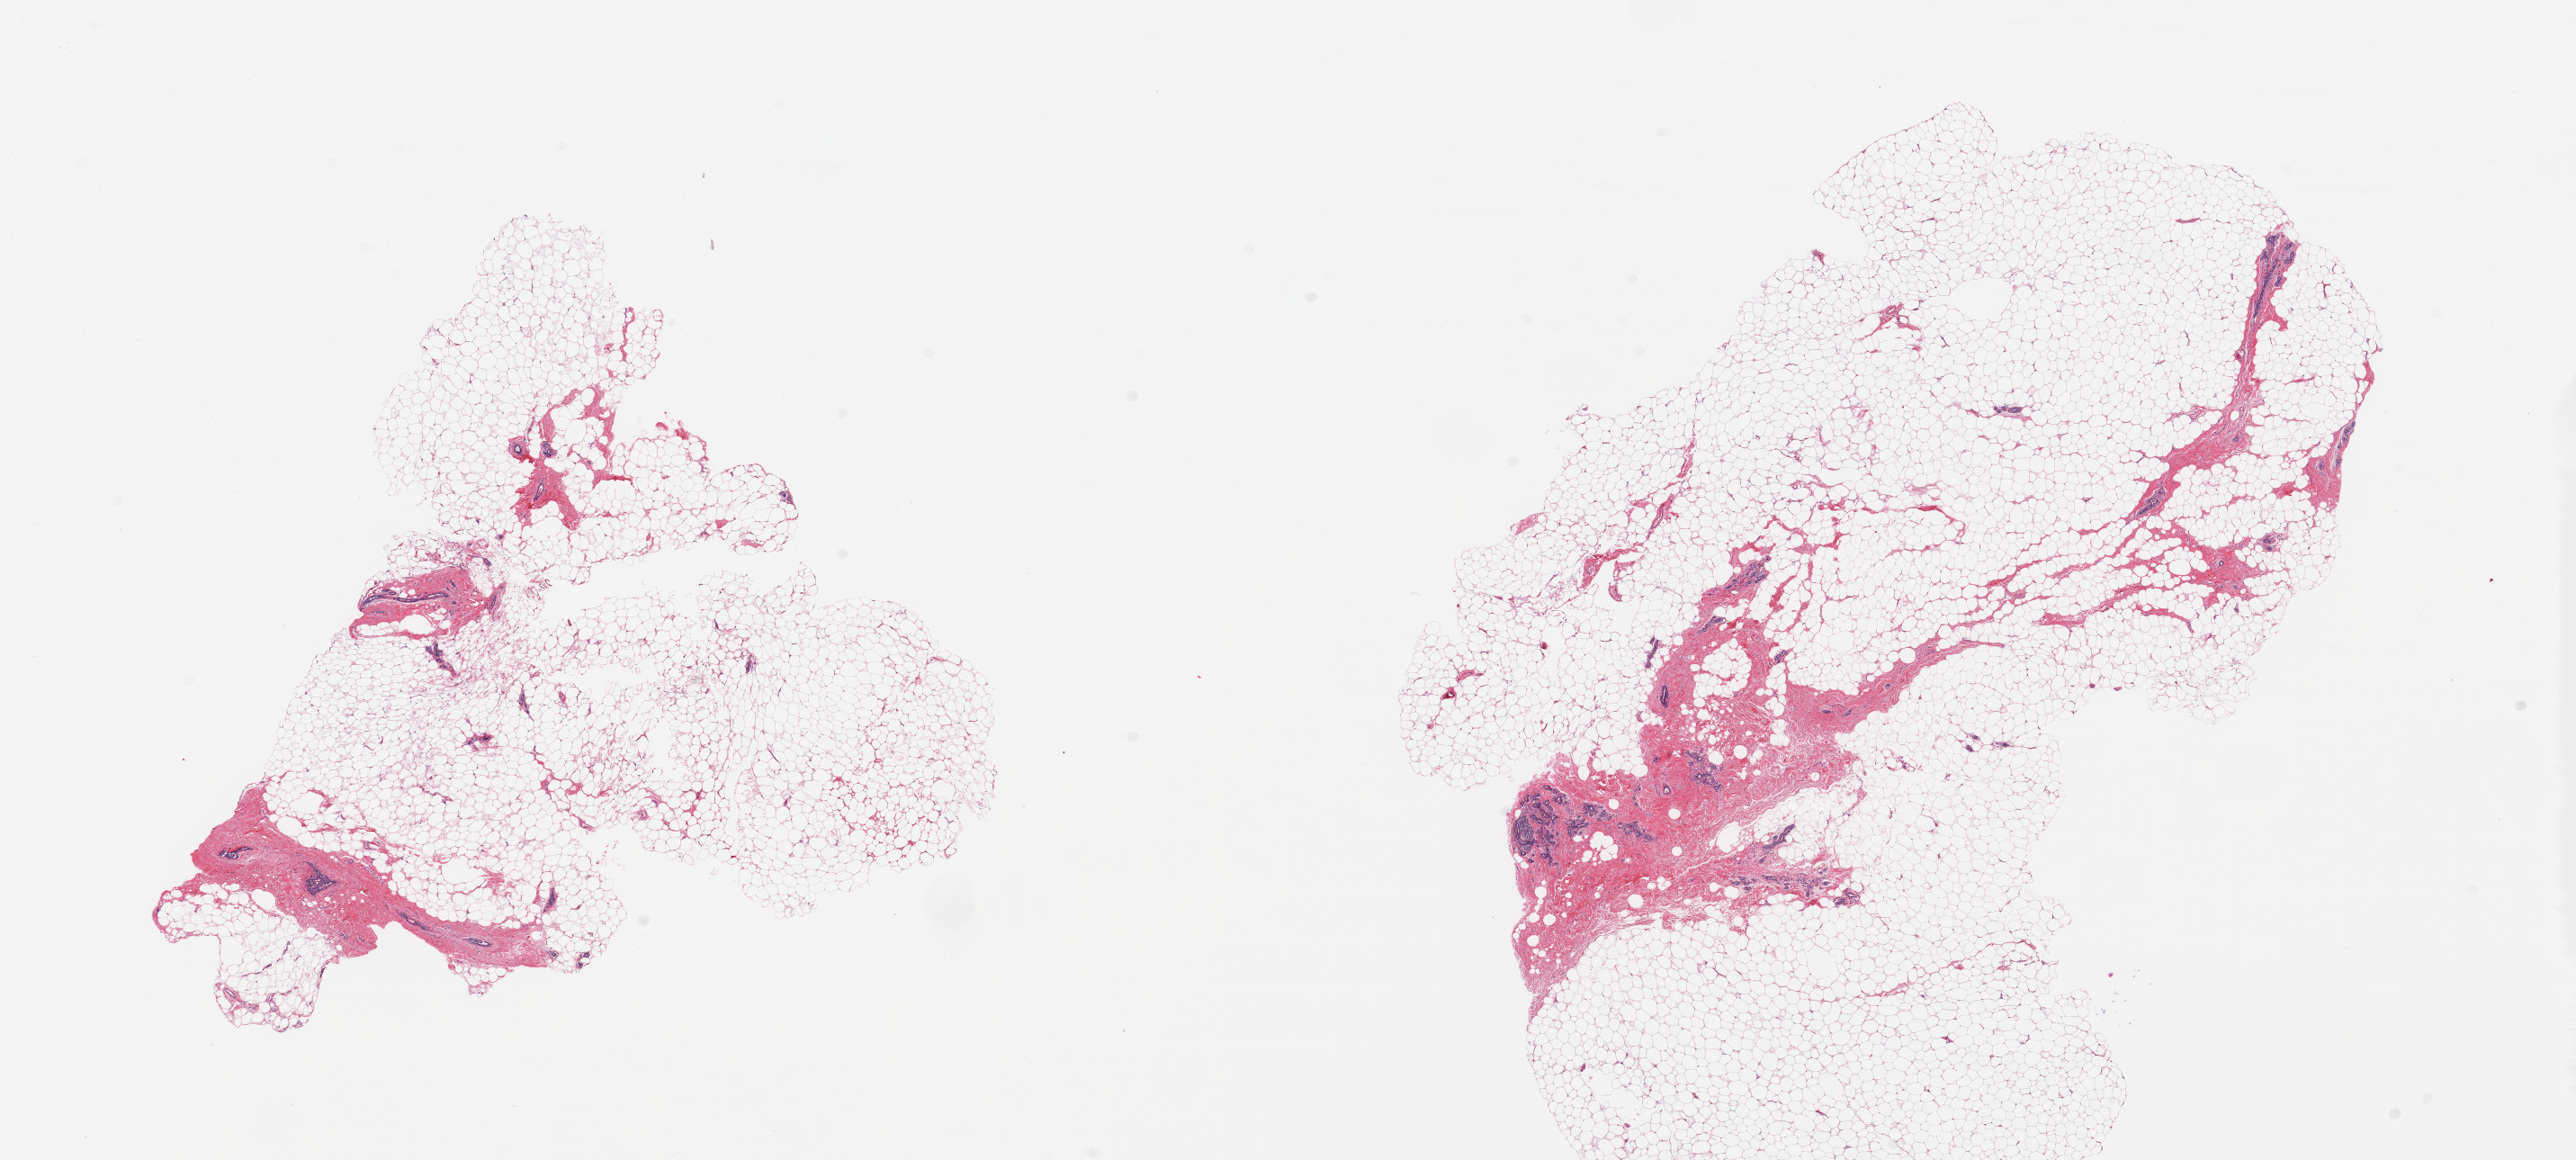
Whole-slide image, H&E stain, a low-resolution overview of the entire scanned area, about 22.6 x 10.2 mm. PAXgene-fixed paraffin-embedded (PFPE) section. Sampled site (target tissue): breast. Tissue donor sample.
Reviewer comment on this tissue sample: 2 pieces mainly fibroadipose elements, few foci of atrophic TDLUs, rep delinated.